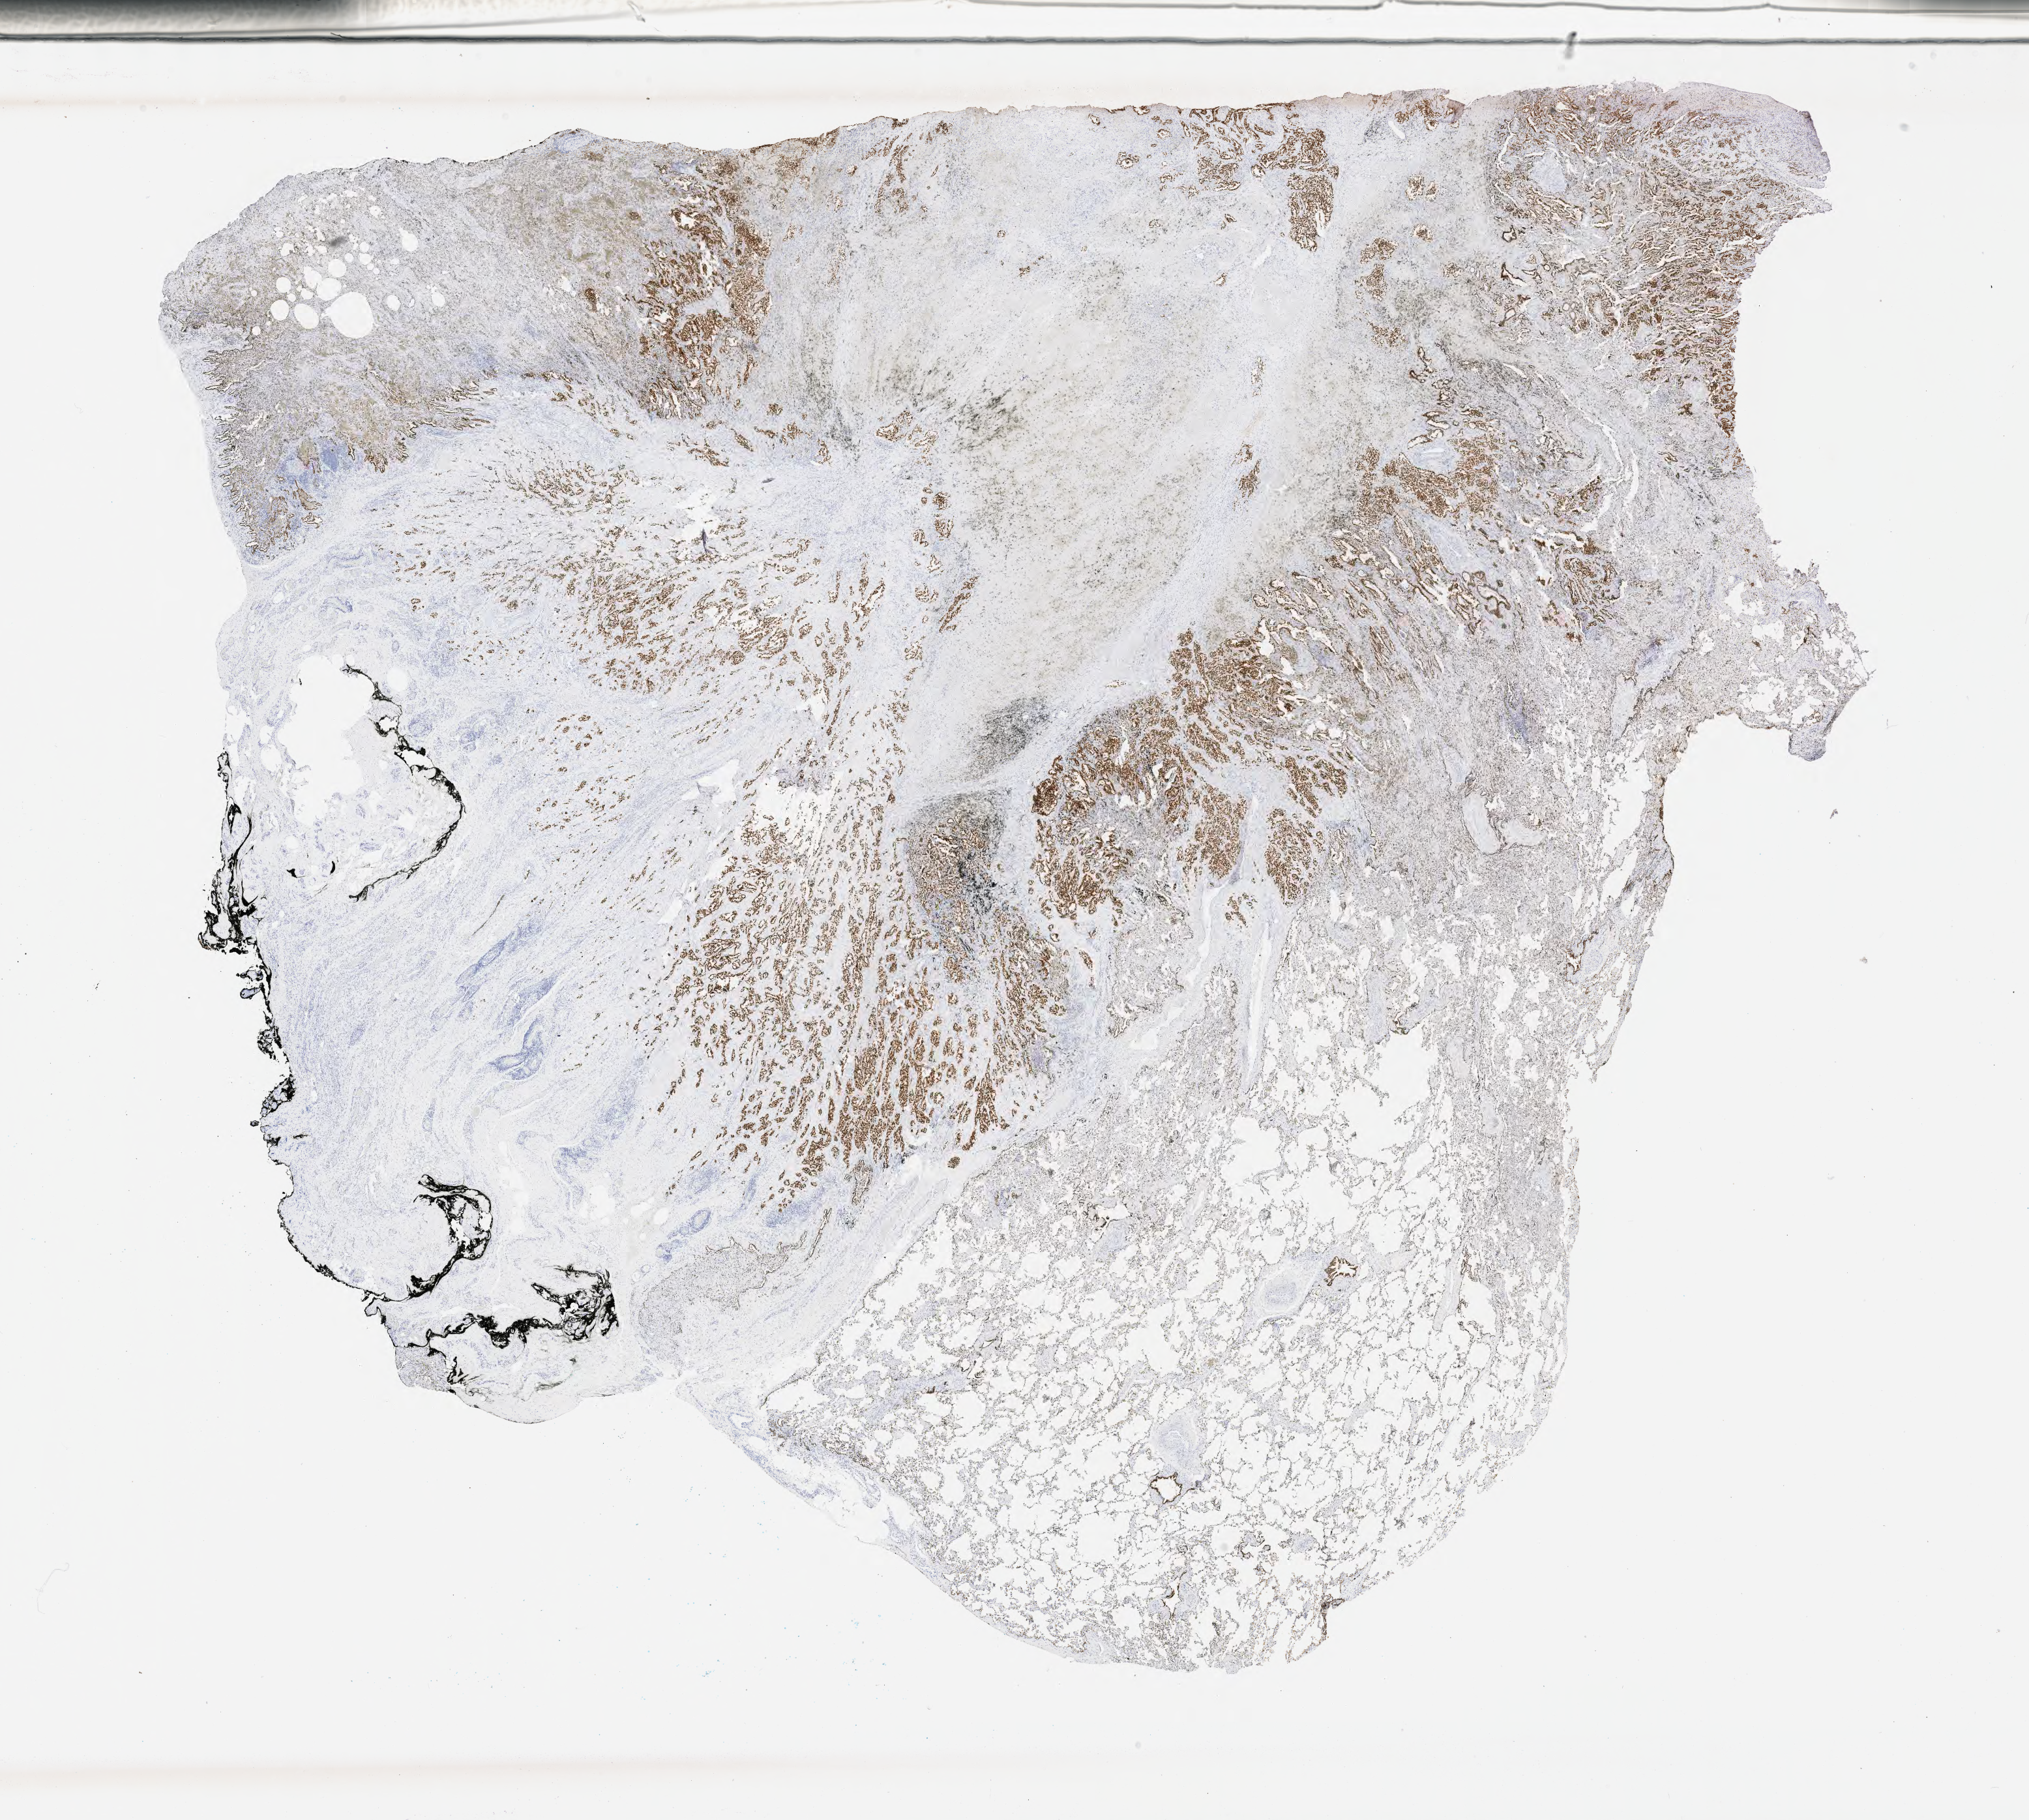
IHC for TTF-1 (thyroid transcription factor 1), whole-slide image, whole scanned area (about 25.1 x 22.6 mm) shown as a low-resolution overview; tumor tissue. Male patient.
Diagnosis: Adenocarcinoma, NOS.